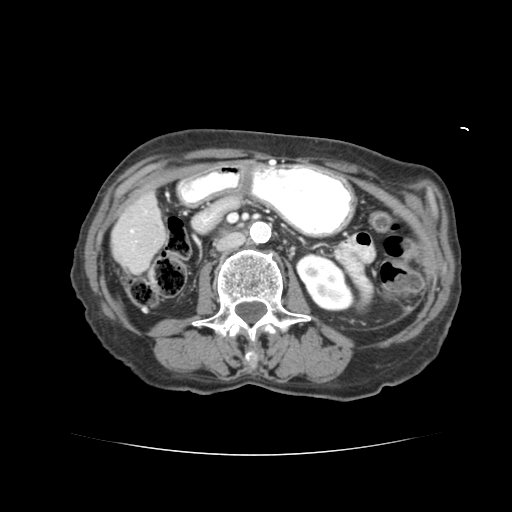
Contrast-enhanced abdominal CT (liver protocol), one axial slice. Position 13 of 77 along the scan axis. Reconstruction kernel STANDARD. 120 kVp. Soft-tissue window (W 400 / L 40 HU). 2.5 mm slice thickness. 512 × 512 image matrix, field of view 340 × 340 mm. From the clinical record (not read from this slice): diagnosis: hepatocellular carcinoma (patient treated with transarterial chemoembolisation; whether this scan precedes or follows treatment is not stated here); TNM stage (as recorded): Stage-I; Child-Pugh class: A; tumour differentiation: well differentiated; tumour nodularity: uninodular.
Structures marked on this image (semi-automatically segmented with operator editing):
- liver parenchyma outside the tumour (the mass and vessels are separate outlines, so this box may not span the whole liver): box from (x=112, y=182) to (x=162, y=270) px
- liver vessels: (x=130, y=208)–(x=154, y=249)